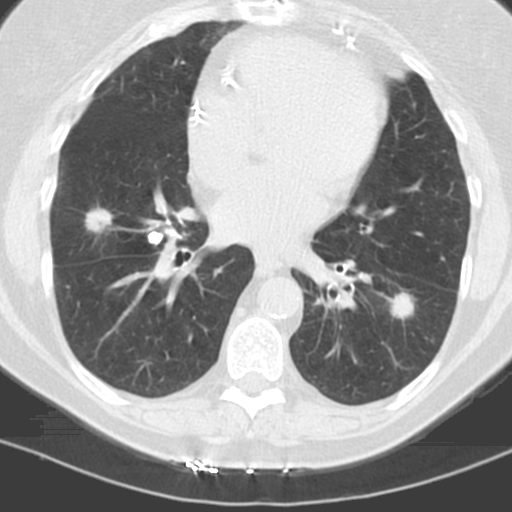
Low-dose screening chest CT, axial slice, baseline annual screen, lung window (W 1500 / L -600 HU). Female participant, aged 60 years at enrolment.
Expert reader's lesion annotation, bounding box <376,286,424,328> (left, top, right, bottom; pixels). The screening reader recorded 3 non-calcified nodules or masses ≥4 mm on this exam (left lower lobe, left lower lobe, right middle lobe); which of them this box marks is not recorded. Official screen result: positive, change unspecified: nodule(s) >= 4 mm or enlarging nodule(s), mass(es), or other non-specific abnormalities suspicious for lung cancer. Lung cancer was diagnosed 96 days after this screen: adenocarcinoma, NOS, left lower lobe, stage IV (AJCC 6th edition), 22 mm at pathology.